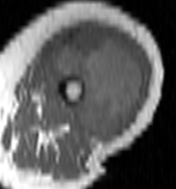
MRI of an extremity soft-tissue mass, one axial slice; MR volume resampled by the dataset authors to the PET/CT grid (not the native acquisition matrix); 3.27 mm slice thickness; 176 × 189 image matrix, field of view 172 × 185 mm. Female patient. From the clinical record (not read from this slice): histological type: undifferentiated – high grade; grade: high; site of the primary tumour: left thigh.
Annotated regions visible in this slice (expert contour drawn on MRI and transferred to this co-registered scan by the dataset authors):
- gross tumour volume including surrounding oedema: box from (x=50, y=27) to (x=145, y=138) px
- gross tumour volume (mass): (x=51, y=27)–(x=143, y=138)